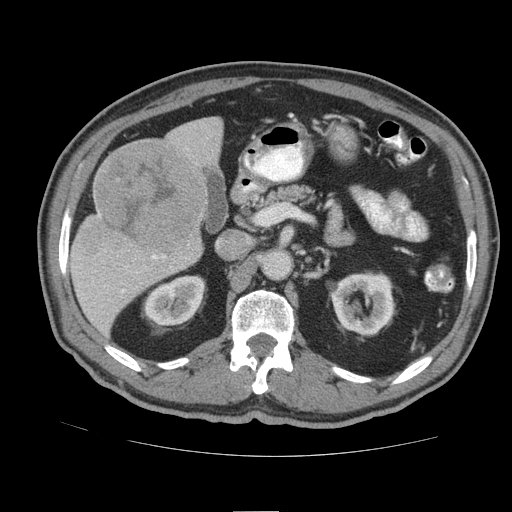
Contrast-enhanced abdominal CT (liver protocol), one axial slice; position 45 of 105 along the scan axis; reconstruction kernel STANDARD; 140 kVp; soft-tissue window (W 400 / L 40 HU); 2.5 mm slice thickness; 512 × 512 image matrix. Case-level facts recorded for this patient, not image findings: diagnosis: hepatocellular carcinoma (patient treated with transarterial chemoembolisation; whether this scan precedes or follows treatment is not stated here); TNM stage (as recorded): Stage-IIIB; Child-Pugh class: A.
Outlined on this slice (semi-automatic segmentation, software-assisted and operator-edited):
- liver parenchyma outside the tumour (the mass and vessels are separate outlines, so this box may not span the whole liver): bounding box (x1, y1, x2, y2) in pixels: (70, 116, 222, 336)
- mass: (94, 141, 203, 252)
- liver vessels: (122, 255, 164, 292)